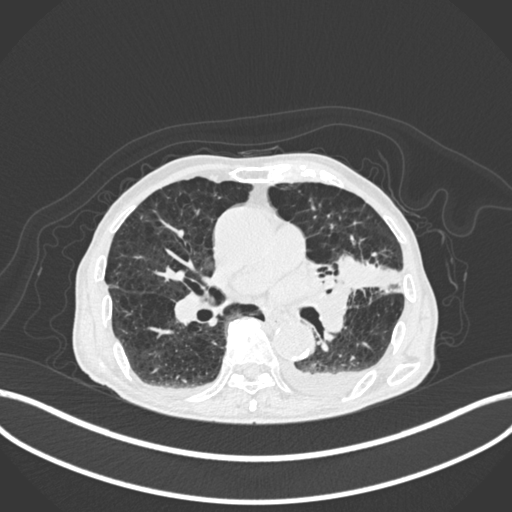
Chest CT, one axial slice. Slice 114 of 400 in the series (ordered by position). Lung window (W 1500 / L -600 HU). 1 mm slice thickness. 512 × 512 image matrix. Patient: male, 90 years or older. Case-level facts recorded for this patient, not image findings: clinical TNM (as recorded): T2b N1 M0.
Outlined on this slice (rectangle marked by the reading radiologist):
- lung tumour (recorded histology: squamous cell carcinoma): box from (x=335, y=254) to (x=401, y=301) px